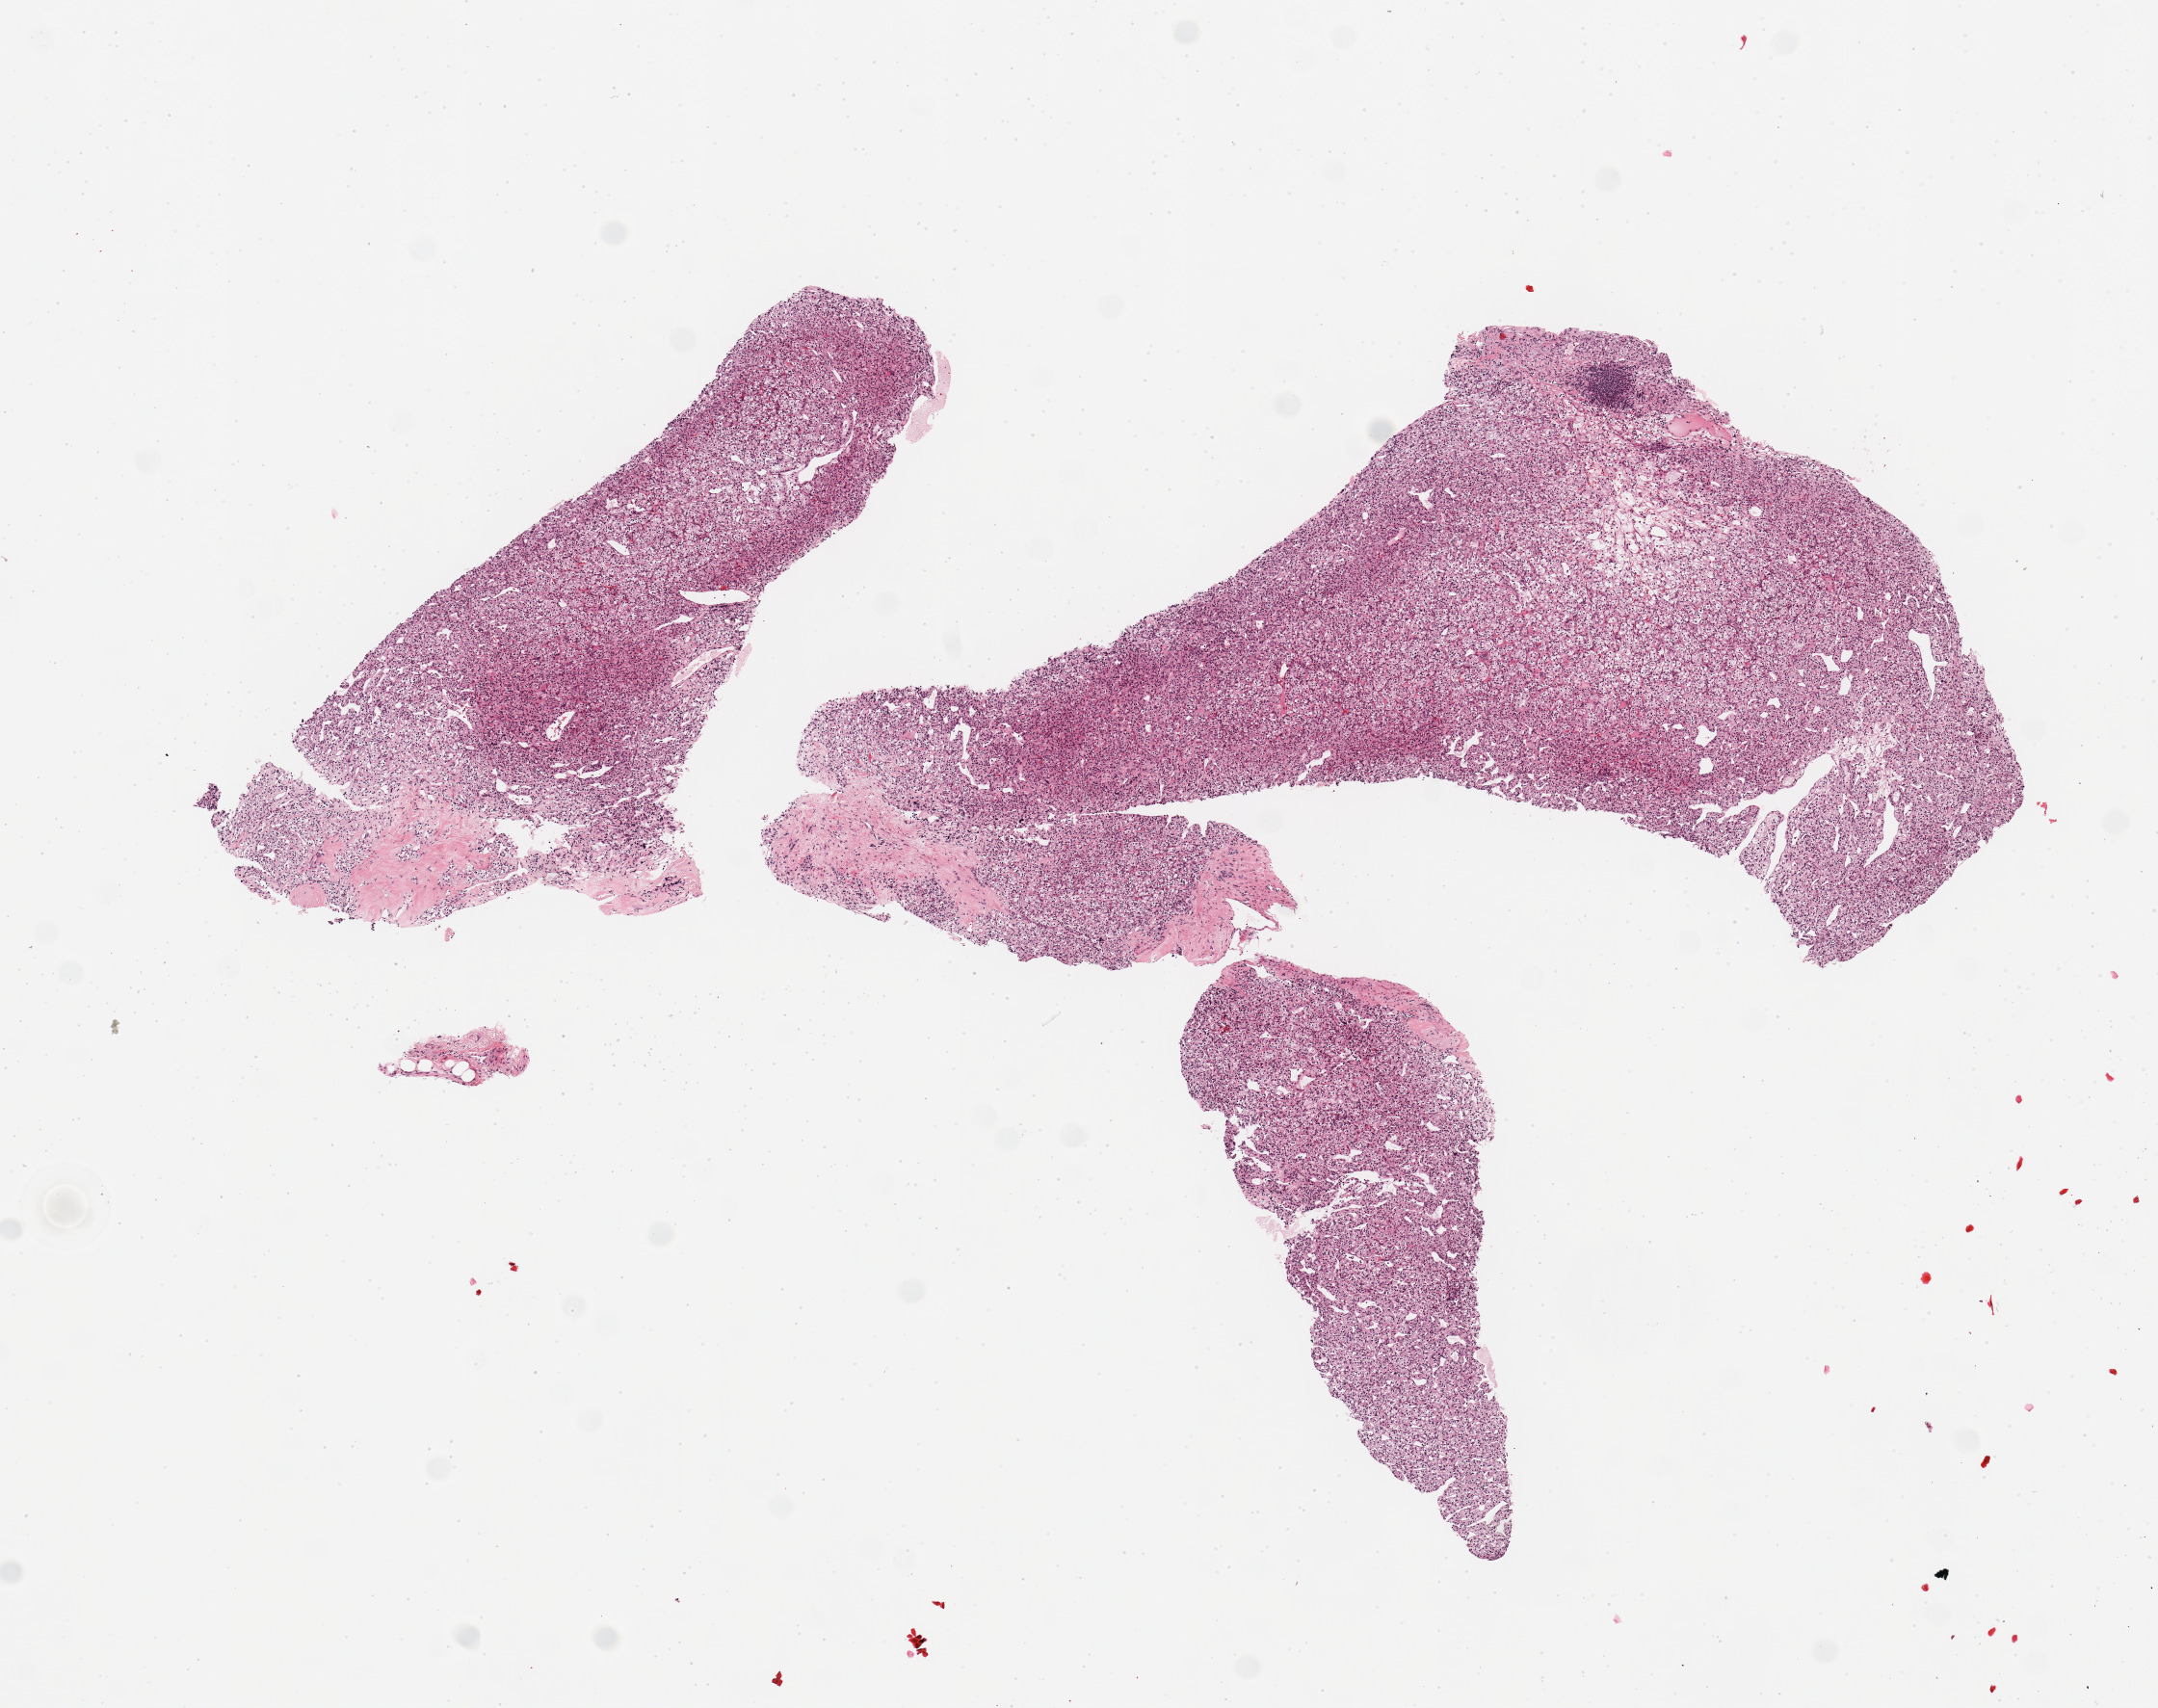
Hematoxylin and eosin (H&E) stained whole-slide image, low-resolution overview of the scanned area, about 8.9 x 7.0 mm (slide scanned at 20x). Tumour tissue sample, sampled site: kidney. Patient: female, age 70 years. Histologic grade: G1 (well differentiated). Slide review estimates, as recorded: tumour nuclei 90%, necrosis 2%.
* histologic diagnosis: Renal cell carcinoma, NOS
* primary tumour site (as recorded): middle
* AJCC pathologic stage: I